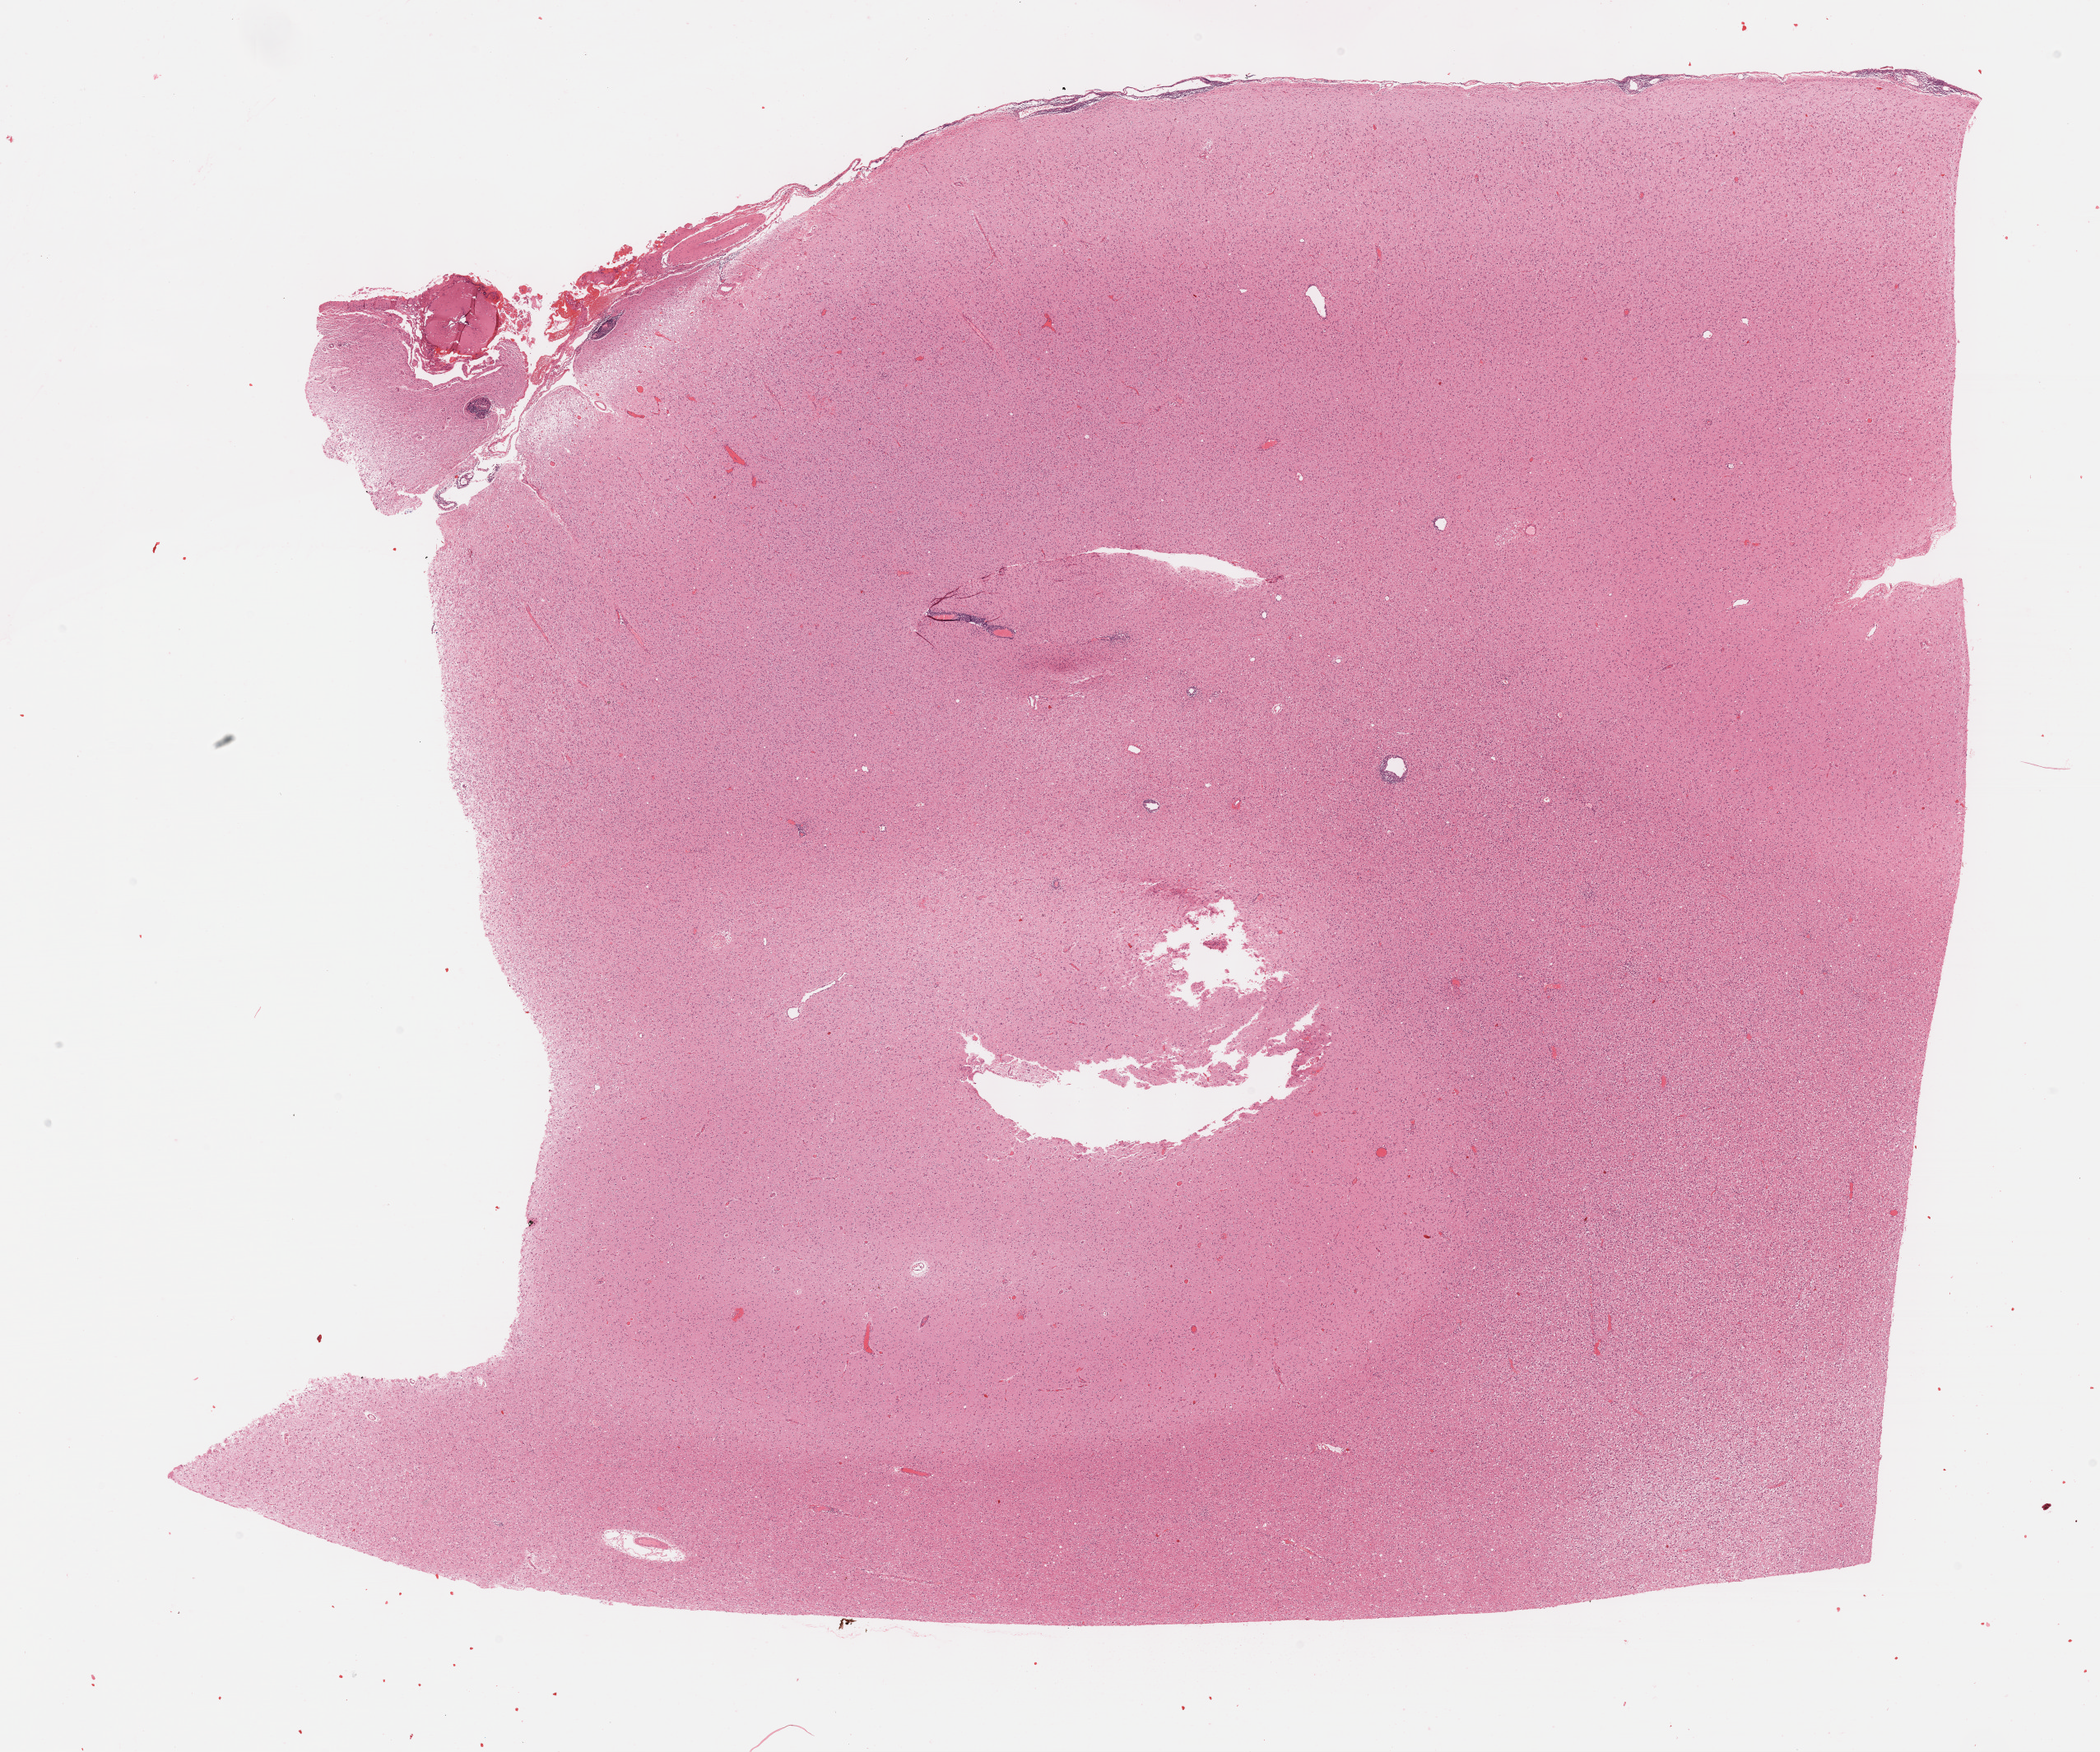
Digitized Hematoxylin and eosin (H&E) stained tissue section (whole slide) — whole scanned area (about 20.6 x 17.2 mm) shown as a low-resolution overview; formalin-fixed paraffin-embedded (FFPE) diagnostic section; primary tumour sample from the brain. Male patient; age at initial diagnosis 48 years. Histologic grade: G3 (poorly differentiated).
Pathologic diagnosis: Astrocytoma, anaplastic (cerebrum).